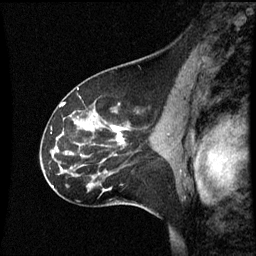
Breast MRI (dynamic contrast-enhanced), one sagittal slice; slice 36 of 60 in the series (ordered by position); dynamic contrast-enhanced series, image 2 of 3 at this slice position (ordered by acquisition); 1.5 T; TE 4.2 ms, TR 8.9 ms; 2 mm slice thickness; 256 × 256 image matrix, field of view 200 × 200 mm. Female patient, age 45 years. Case-level facts recorded for this patient, not image findings: setting: breast cancer imaged before/during neoadjuvant chemotherapy; receptor status: HR-positive, HER2-negative.
Outlined on this slice (semi-automatic segmentation, software-assisted and operator-edited):
- analysis volume of interest (the breast-tissue region the enhancement analysis was run in; not a lesion): box from (x=46, y=94) to (x=171, y=205) px
- tumour enhancement mask (voxels above the 70 % enhancement threshold inside the analysis volume of interest): (x=110, y=126)–(x=127, y=143)